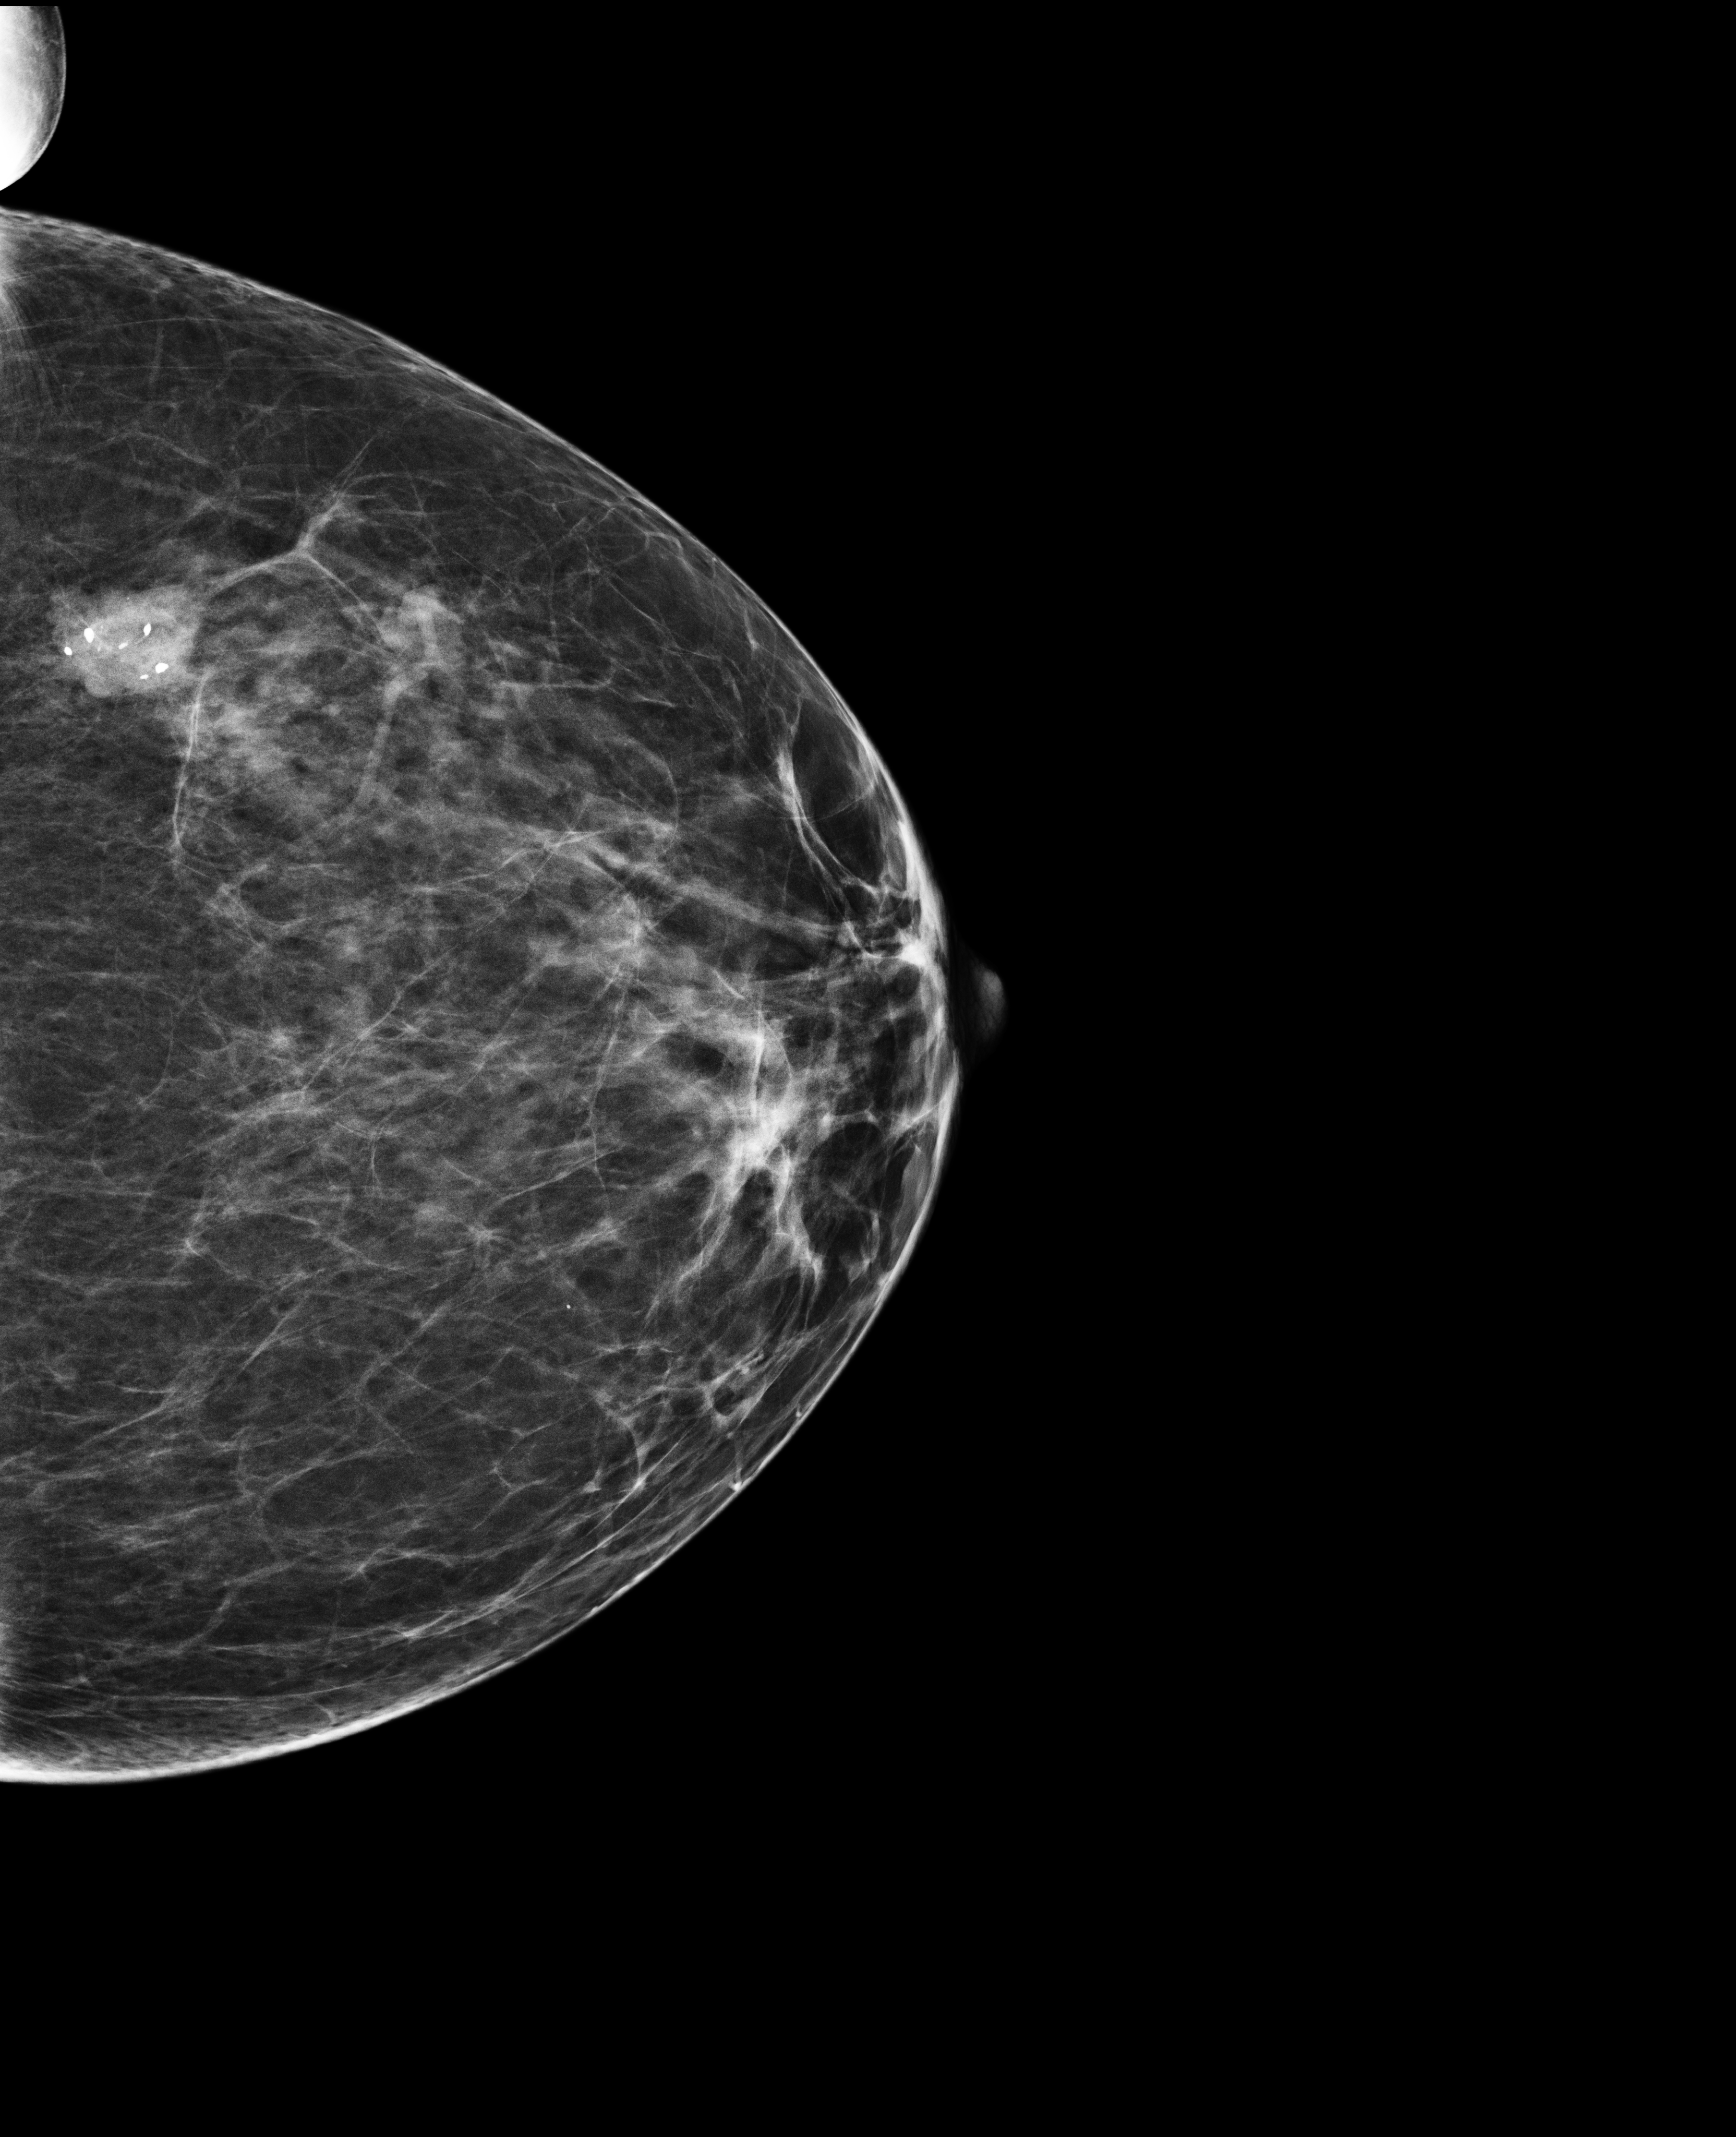
Screening examination. Female patient, age 65 years.
Image type: full-field digital mammogram. Breast: left. Projection: CC view.